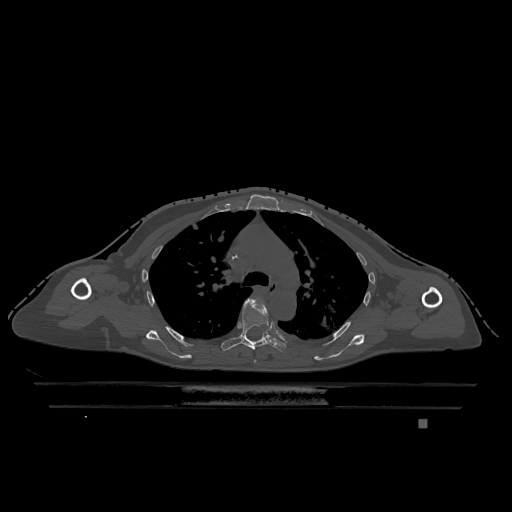
CT including the spine, one axial slice; slice 845 of 1317 in the series (ordered by position); bone window (W 1800 / L 400 HU); 0.5 mm slice thickness; 512 × 512 image matrix. Patient: female, 74 years. From the clinical record (not read from this slice): primary cancer: lung; vertebrae with lytic lesions (as recorded): T1, T4, T5, T6, L4, L5.
Outlined on this slice (semi-automatic segmentation, software-assisted and operator-edited):
- T4 vertebra: bounding box (x1, y1, x2, y2) in pixels: (254, 360, 256, 363)
- T5 vertebra: (221, 298, 287, 353)